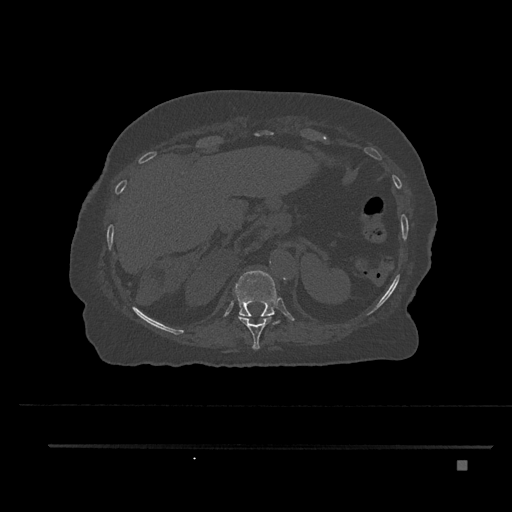
CT including the spine, one axial slice; position 331 of 797 along the scan axis; reconstruction kernel Br40s/3; 120 kVp; bone window (W 1800 / L 400 HU); 0.5 mm slice thickness; 512 × 512 image matrix. Female patient, age 76 years. Case-level facts recorded for this patient, not image findings: primary cancer: lung; vertebrae with lytic lesions (as recorded): T11, L3.
Annotated regions visible in this slice (semi-automatic segmentation, software-assisted and operator-edited):
- T10 vertebra: box from (x=238, y=316) to (x=272, y=350) px
- T11 vertebra: (x=234, y=270)–(x=279, y=325)